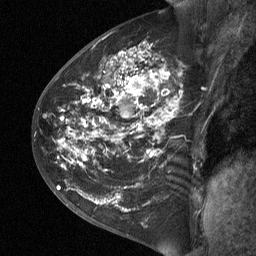
Breast MRI (dynamic contrast-enhanced), one sagittal slice. Position 32 of 64 along the scan axis. Dynamic contrast-enhanced study with each time point stored as its own series, time point 2 of 3 at this slice position (early post-contrast, ordered by acquisition time). 1.5 T. TE 4.8 ms, TR 27 ms. 2 mm slice thickness. 256 × 256 image matrix, field of view 200 × 200 mm. Female patient, age 42 years. Case-level facts recorded for this patient, not image findings: setting: breast cancer imaged before/during neoadjuvant chemotherapy; receptor status: triple-negative.
Annotated regions visible in this slice (semi-automatically segmented with operator editing):
- analysis volume of interest (the breast-tissue region the enhancement analysis was run in; not a lesion): bounding box (x1, y1, x2, y2) in pixels: (43, 29, 201, 190)
- tumour enhancement mask (voxels above the 90 % enhancement threshold inside the analysis volume of interest): (69, 50, 180, 164)